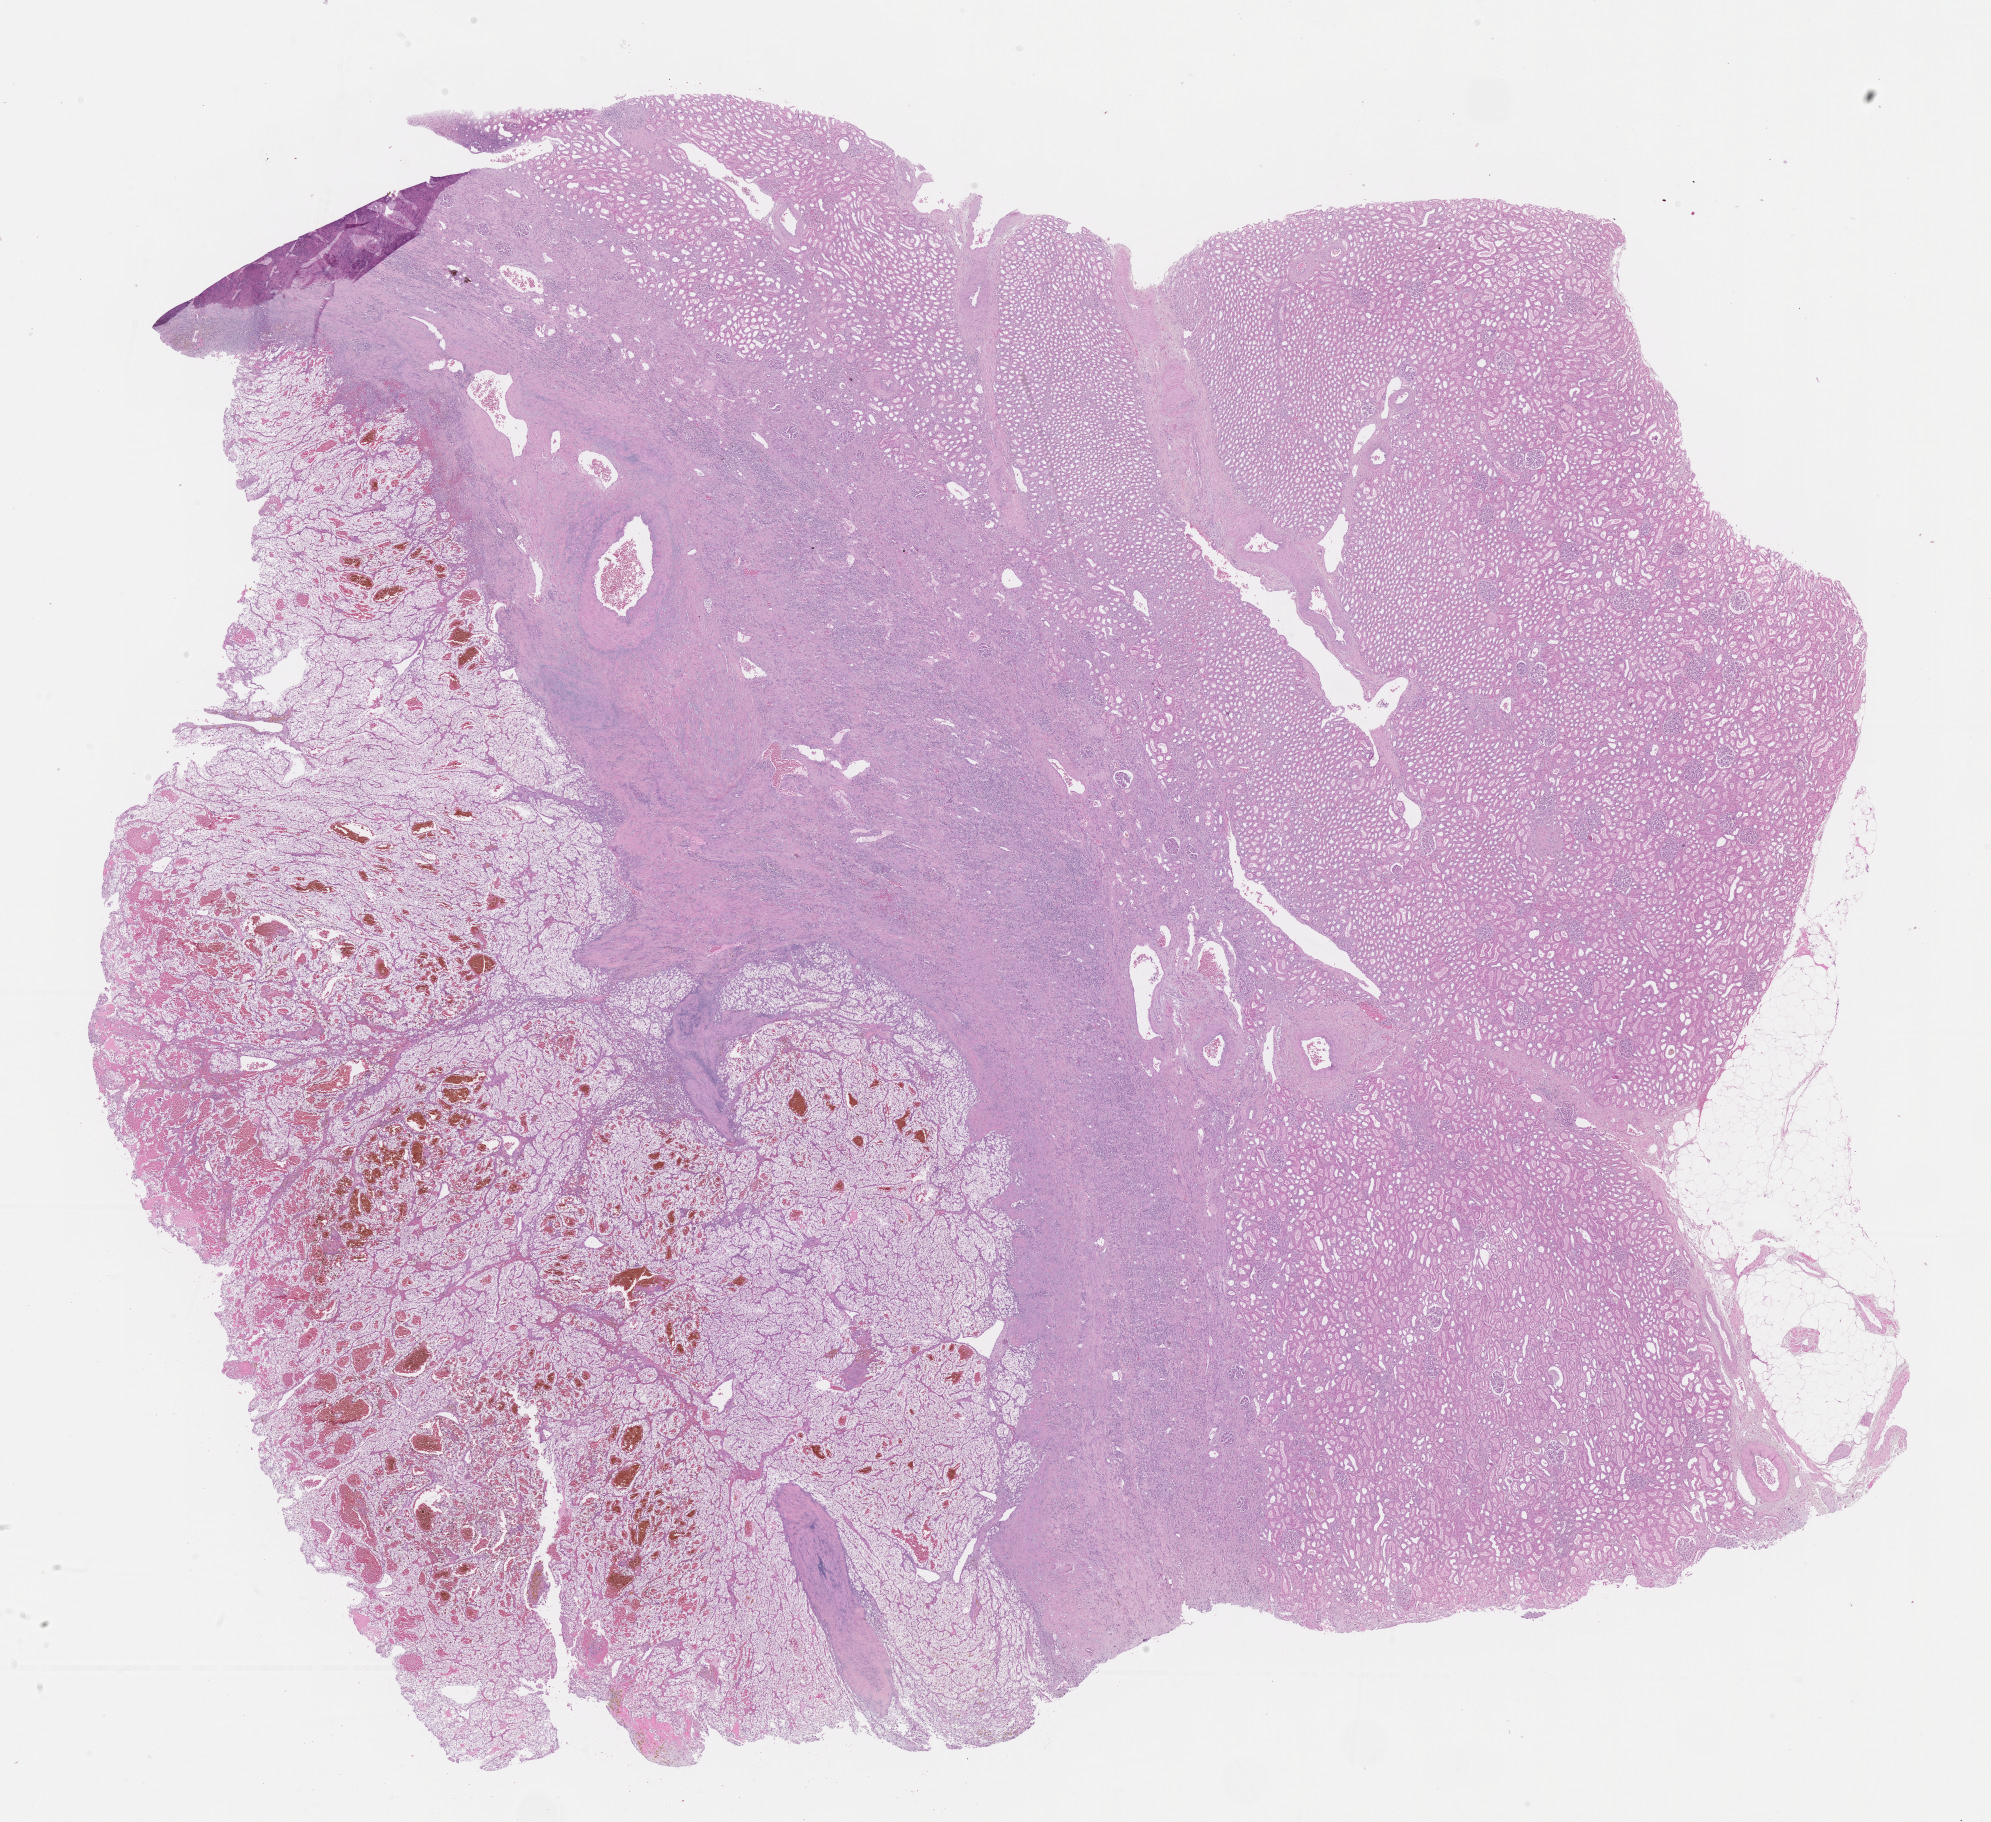
Digitized H&E-stained tissue section (whole slide) — low-resolution overview of the scanned area, about 16.1 x 14.7 mm, formalin-fixed paraffin-embedded (FFPE) diagnostic section, kidney, primary tumour sample. Patient: male, age at initial diagnosis 38 years.
Histologic diagnosis: Clear cell adenocarcinoma, NOS.